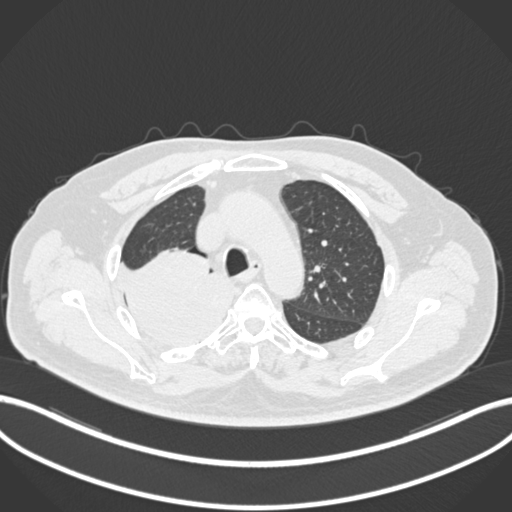
Chest CT, one axial slice; slice 154 of 218 in the series (ordered by position); reconstruction kernel B30f; 120 kVp; lung window (W 1500 / L -600 HU); 1 mm slice thickness; 512 × 512 image matrix, field of view 400 × 400 mm. Male patient, age 68 years. Case-level facts recorded for this patient, not image findings: clinical TNM (as recorded): T2a N0 M0.
Structures marked on this image (bounding box drawn by a radiologist):
- lung tumour (recorded histology: adenocarcinoma): bounding box <113,244,232,350> (left, top, right, bottom; pixels)